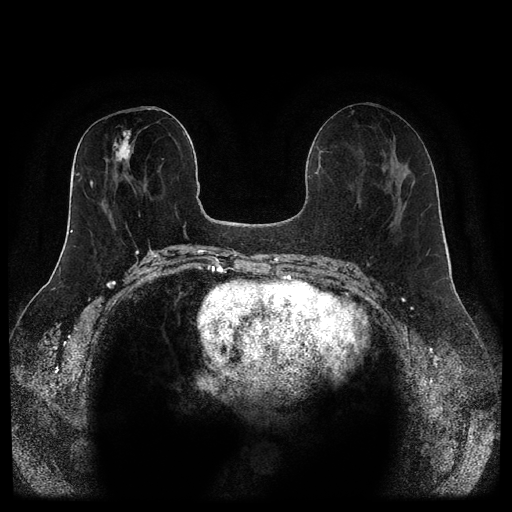
Breast MRI (dynamic contrast-enhanced, multi-phase), one axial slice; position 48 of 116 along the scan axis; dynamic contrast-enhanced series, time point 2 of 5 at this slice position (early post-contrast); 1.5 T; TE 2.6 ms, TR 5.3 ms; 2 mm slice thickness; 512 × 512 image matrix. Patient: female, 46 years.
Annotated regions visible in this slice (semi-automatically segmented with operator editing):
- breast lesion (labelled 'tumour' in the annotation; benign lesions carry a separate 'benign' label): box from (x=112, y=129) to (x=135, y=166) px